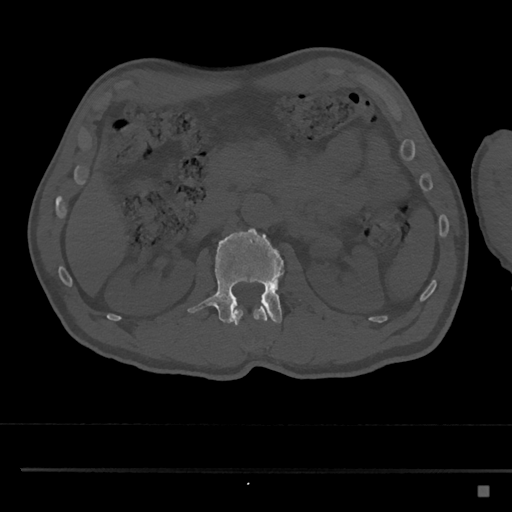
CT including the spine, one axial slice. Position 780 of 797 along the scan axis. 120 kVp. Bone window (W 1800 / L 400 HU). 512 × 512 image matrix, field of view 391 × 391 mm. Patient: male, 59 years. Case-level facts recorded for this patient, not image findings: primary cancer: prostate.
Annotated regions visible in this slice (semi-automatically segmented with operator editing):
- L1 vertebra: bounding box [x1, y1, x2, y2] px = [232, 306, 269, 325]
- L2 vertebra: [188, 228, 301, 324]